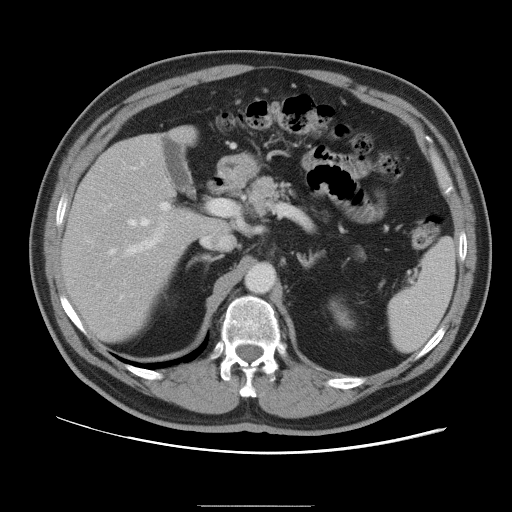
Contrast-enhanced abdominal CT, one axial slice; slice 58 of 105 in the series (ordered by position); 120 kVp; intravenous contrast given; soft-tissue window (W 400 / L 40 HU); 5 mm slice thickness; 512 × 512 image matrix, field of view 399 × 399 mm. Male patient, age 64 years. From the clinical record (not read from this slice): diagnosis: colorectal cancer liver metastases, imaged before liver resection; multiple liver metastases: yes; largest metastasis: 3 cm; disease in both lobes: yes.
Annotated regions visible in this slice (expert manual segmentation):
- hepatic veins: box from (x=110, y=163) to (x=149, y=254) px
- liver: (x=63, y=136)–(x=215, y=342)
- planned liver remnant (the part of the liver to remain after resection): (x=63, y=136)–(x=218, y=341)
- portal vein (with intrahepatic branches): (x=125, y=202)–(x=170, y=314)